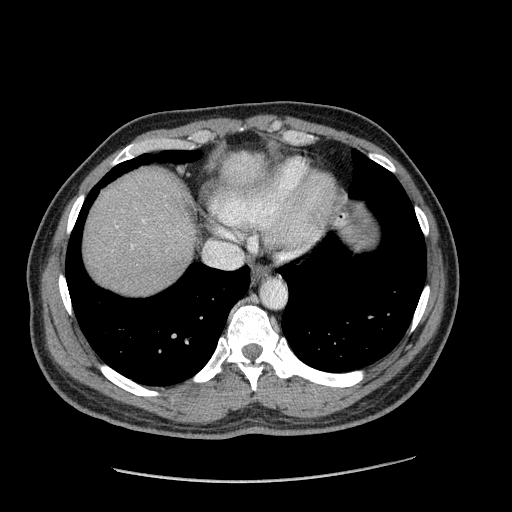
Contrast-enhanced abdominal CT (liver protocol), one axial slice; position 161 of 182 along the scan axis; soft-tissue window (W 400 / L 40 HU); 512 × 512 image matrix, field of view 400 × 400 mm. From the clinical record (not read from this slice): diagnosis: hepatocellular carcinoma (patient treated with transarterial chemoembolisation; whether this scan precedes or follows treatment is not stated here); TNM stage (as recorded): Stage-I; Child-Pugh class: A; tumour differentiation: well differentiated.
Outlined on this slice (semi-automatically segmented with operator editing):
- abdominal aorta: bounding box (x1, y1, x2, y2) in pixels: (261, 279, 287, 308)
- liver parenchyma outside the tumour (the mass and vessels are separate outlines, so this box may not span the whole liver): (84, 168, 194, 294)